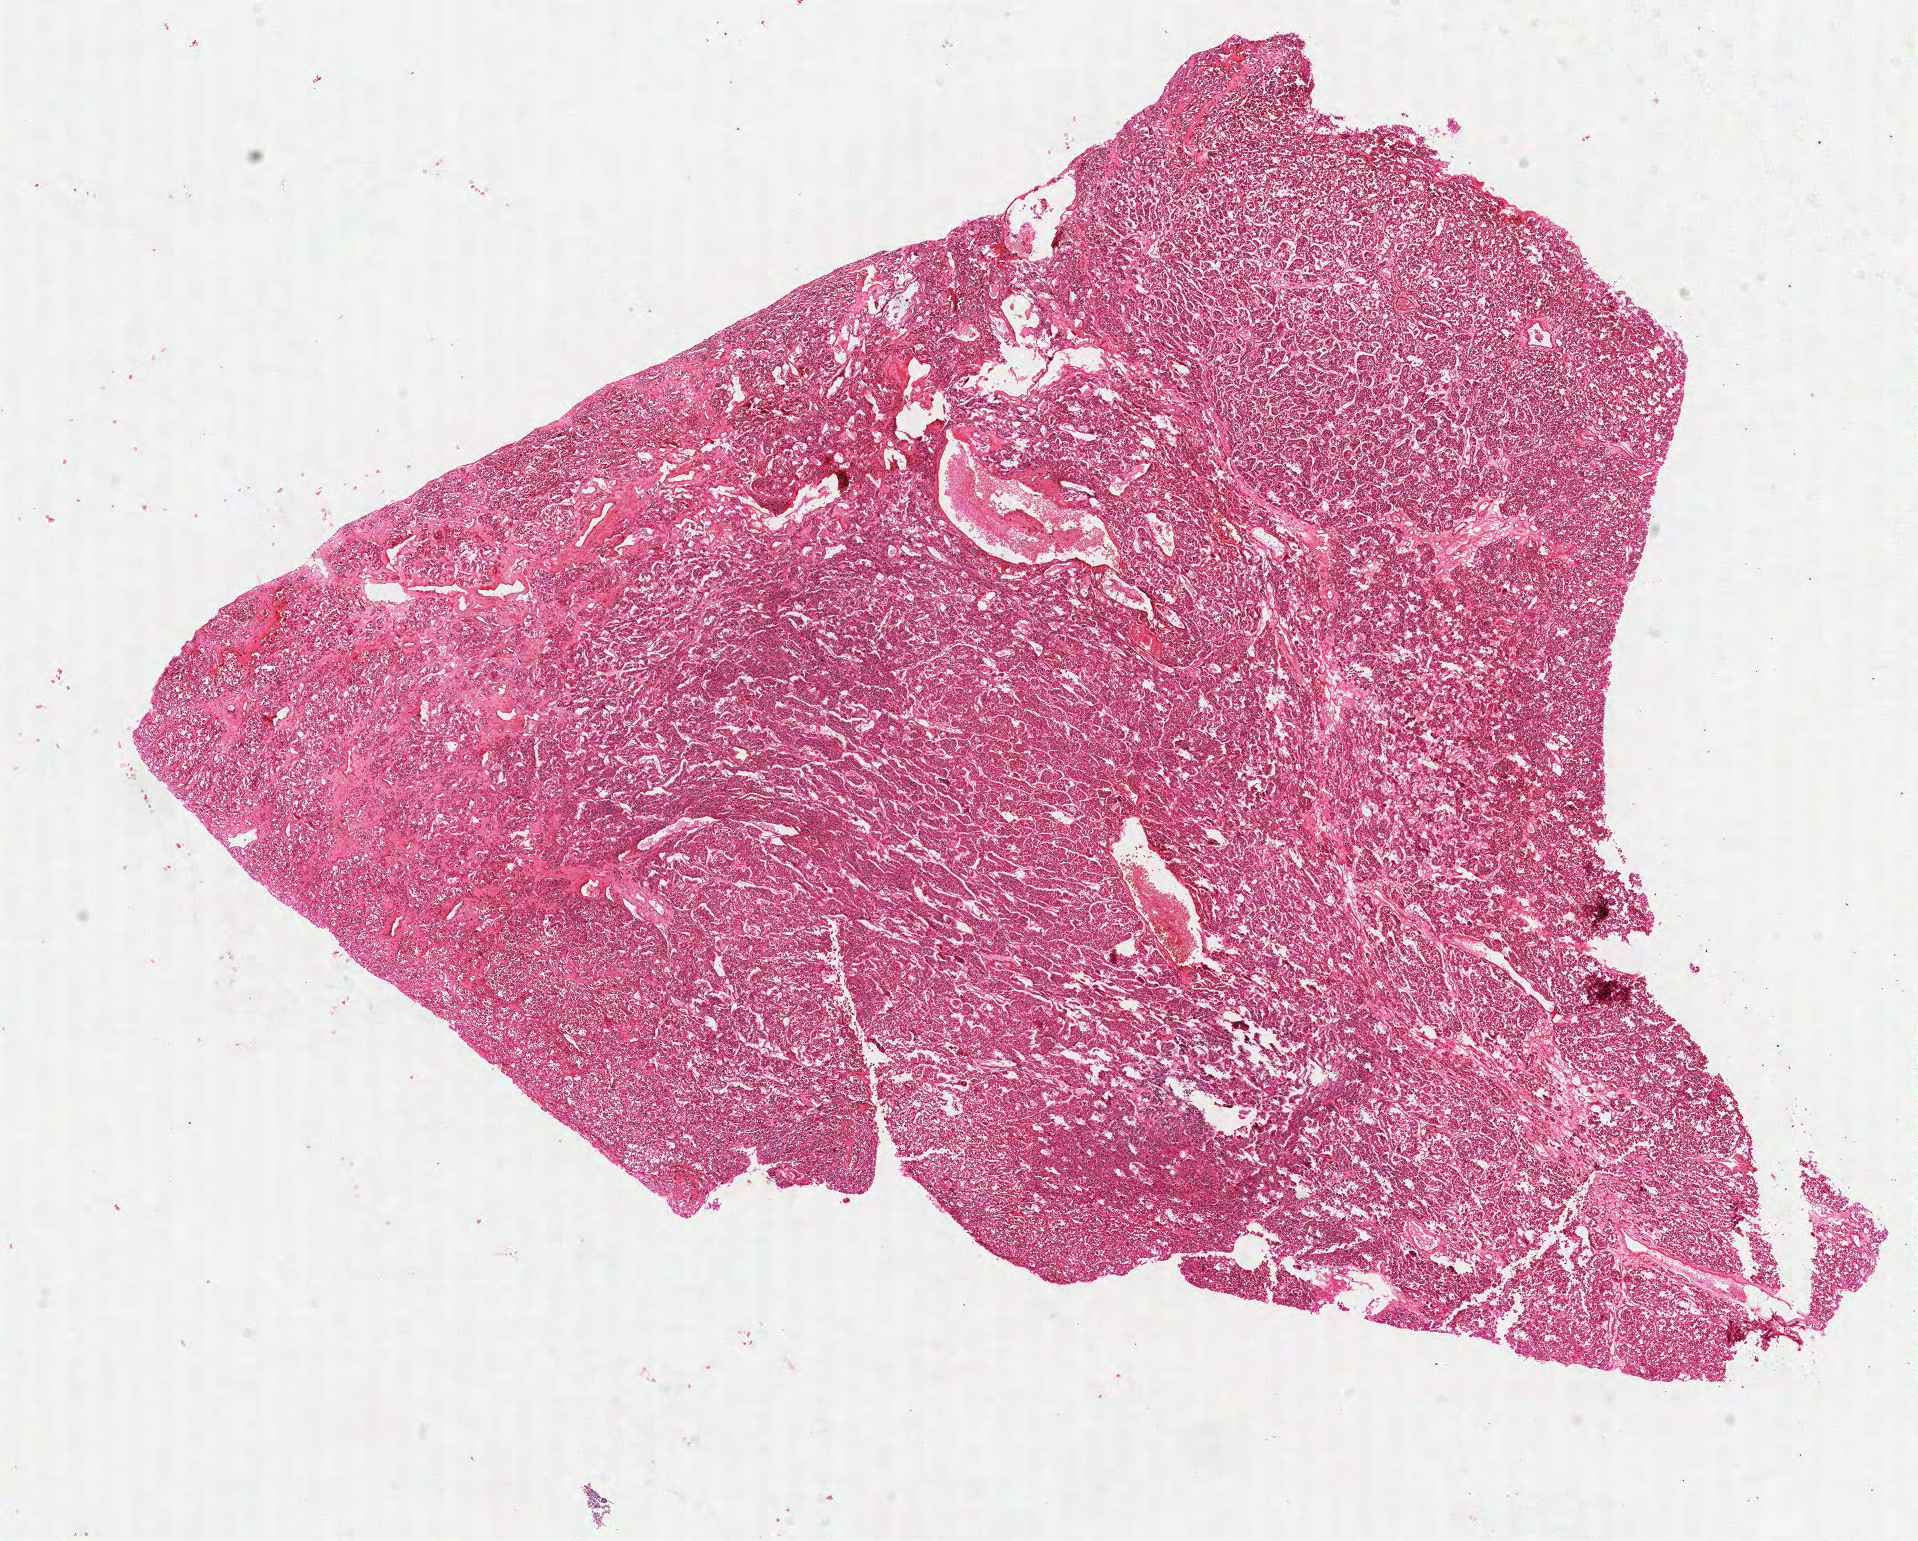
Digitized H&E-stained tissue section (whole slide) — low-resolution overview of the scanned area, about 15.5 x 12.4 mm (from a 40x scan), FFPE section, primary tumour sample from the kidney. Male, age 65 years at initial diagnosis. Histologic grade: GX (grade cannot be assessed).
Histologic diagnosis: Clear cell adenocarcinoma, NOS. AJCC pathologic stage: I.